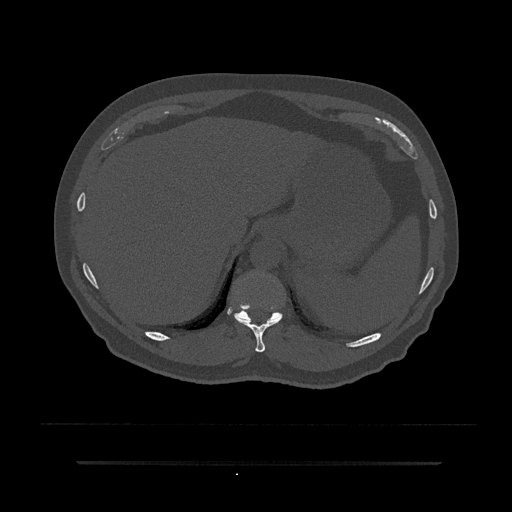
CT including the spine, one axial slice. Position 301 of 797 along the scan axis. Bone window (W 1800 / L 400 HU). 0.5 mm slice thickness. 512 × 512 image matrix, field of view 464 × 464 mm. Patient: male, 59 years. From the clinical record (not read from this slice): primary cancer: bile ducts.
Outlined on this slice (semi-automatic segmentation, software-assisted and operator-edited):
- T10 vertebra: bounding box <235,316,282,353> (left, top, right, bottom; pixels)
- T11 vertebra: <229,302,283,321>